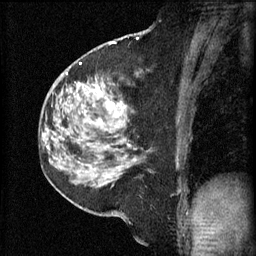
Breast MRI (dynamic contrast-enhanced), one sagittal slice. Slice 30 of 60 in the series (ordered by position). 3 images stored at this slice position (order not interpretable as contrast timing). 1.5 T. TE 4.2 ms, TR 11 ms. 2.3 mm slice thickness. 256 × 256 image matrix, field of view 180 × 180 mm. Female patient, age 52 years.
Outlined on this slice (semi-automatically segmented with operator editing):
- analysis volume of interest (the breast-tissue region the enhancement analysis was run in; not a lesion): box from (x=86, y=76) to (x=134, y=157) px
- tumour enhancement mask (voxels above the 70 % enhancement threshold inside the analysis volume of interest): (x=108, y=102)–(x=125, y=109)